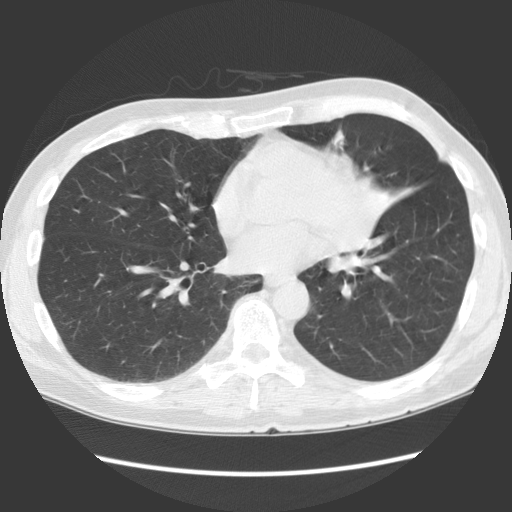
Low-dose screening chest CT, one axial slice; slice 60 of 136 in the series (ordered by position); 140 kVp; lung window (W 1500 / L -600 HU); 2.5 mm slice thickness; 512 × 512 image matrix, field of view 360 × 360 mm.
Outlined on this slice (manually delineated by an expert):
- lesion 1 (tumor, hilum of left lung): bounding box <358,176,392,214> (left, top, right, bottom; pixels)